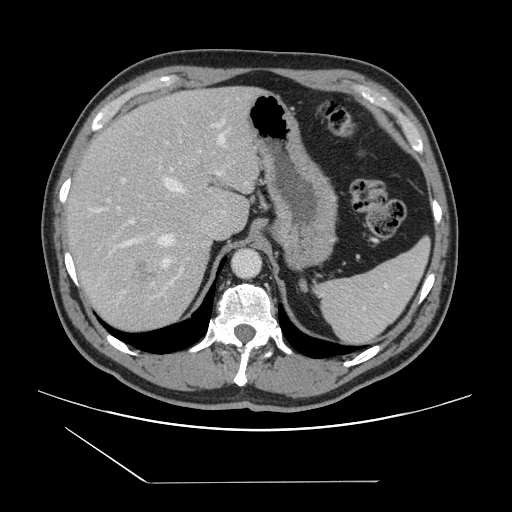
Contrast-enhanced abdominal CT, one axial slice. Position 107 of 157 along the scan axis. 120 kVp. Intravenous contrast given. Soft-tissue window (W 400 / L 40 HU). 512 × 512 image matrix, field of view 407 × 407 mm. Male patient, age 61 years. From the clinical record (not read from this slice): diagnosis: colorectal cancer liver metastases, imaged before liver resection; multiple liver metastases: yes; largest metastasis: 5.5 cm; chemotherapy before resection: no.
Outlined on this slice (manually delineated by an expert):
- hepatic veins: bounding box (x1, y1, x2, y2) in pixels: (92, 133, 225, 269)
- liver: (67, 87, 259, 333)
- planned liver remnant (the part of the liver to remain after resection): (66, 87, 237, 230)
- portal vein (with intrahepatic branches): (108, 141, 223, 284)
- liver metastasis: (126, 254, 174, 313)